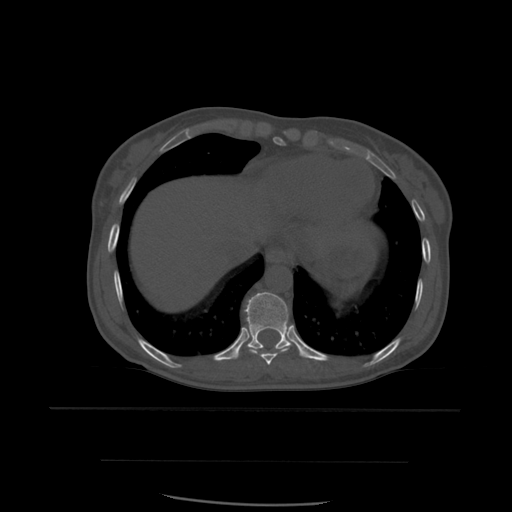
CT including the spine, one axial slice. Position 325 of 574 along the scan axis. Bone window (W 1800 / L 400 HU). 512 × 512 image matrix, field of view 392 × 392 mm. Patient age 48 years. Case-level facts recorded for this patient, not image findings: primary cancer: lung.
Outlined on this slice (semi-automatically segmented with operator editing):
- T10 vertebra: box from (x=239, y=292) to (x=302, y=357) px
- T9 vertebra: (x=246, y=344)–(x=293, y=366)